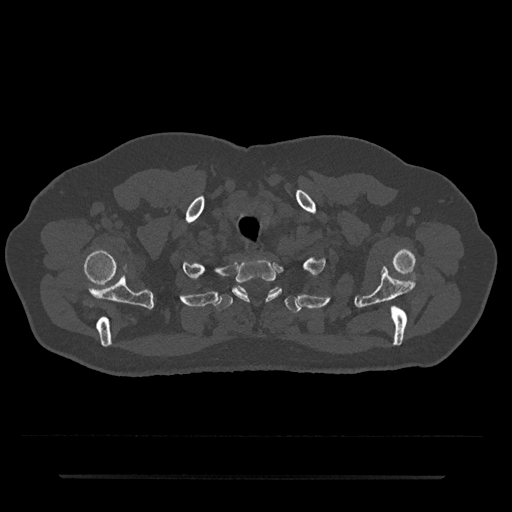
CT including the spine, one axial slice; slice 629 of 797 in the series (ordered by position); reconstruction kernel Br40s/3; 120 kVp; bone window (W 1800 / L 400 HU); 512 × 512 image matrix, field of view 437 × 437 mm. Patient: male, 69 years. From the clinical record (not read from this slice): primary cancer: prostate.
Annotated regions visible in this slice (semi-automatic segmentation, software-assisted and operator-edited):
- T1 vertebra: bounding box [x1, y1, x2, y2] px = [232, 259, 282, 301]
- T2 vertebra: [216, 287, 301, 313]